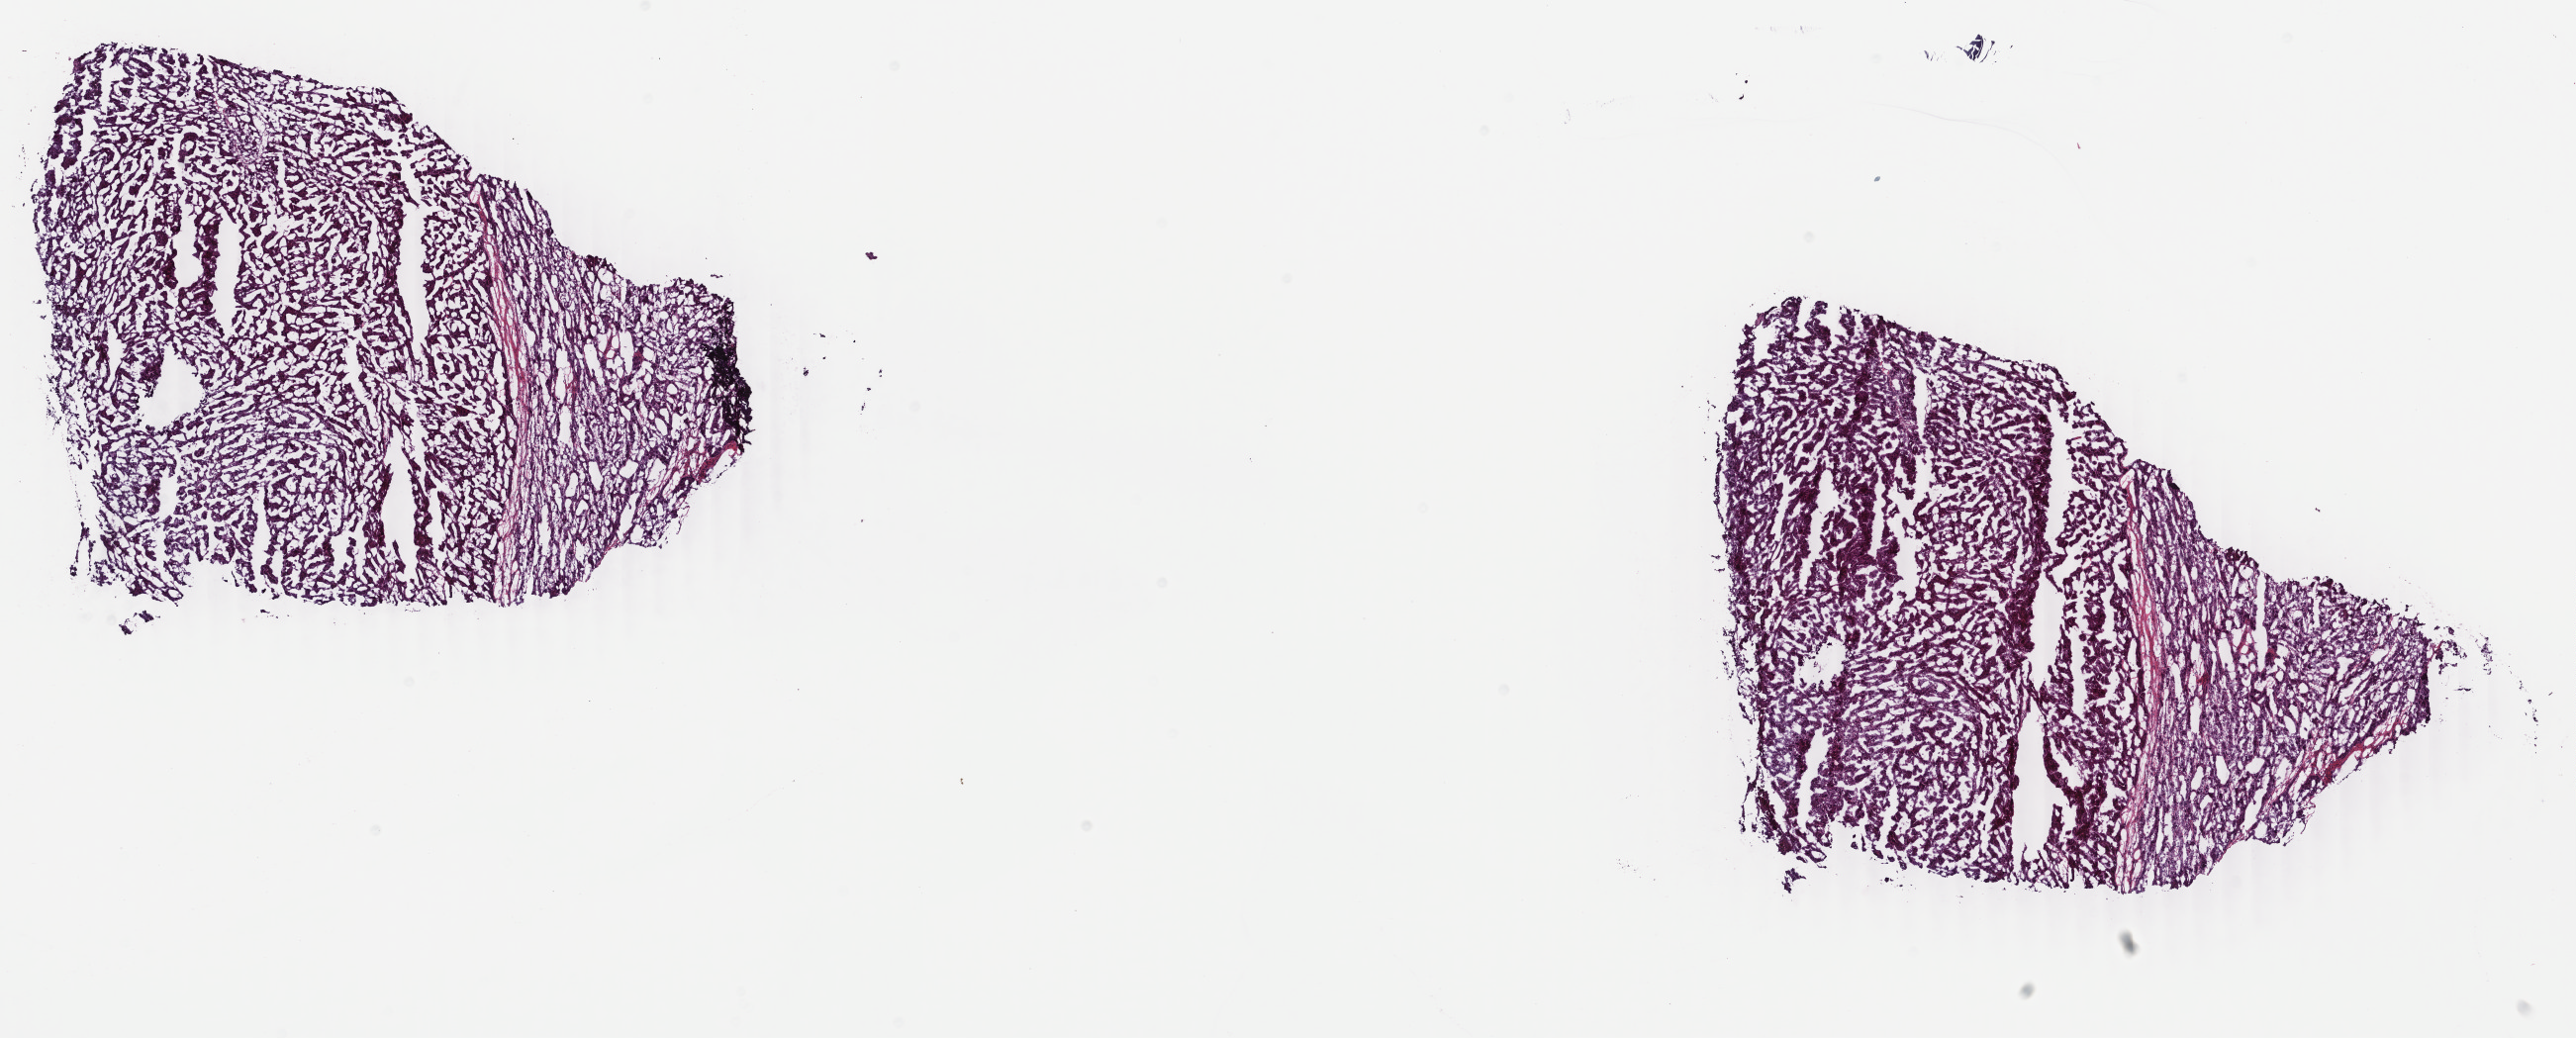
Hematoxylin and eosin (H&E) stained whole-slide image — whole scanned area (about 20.7 x 8.3 mm) shown as a low-resolution overview, frozen section, primary tumour sample from the liver. Male patient; age at initial diagnosis 68 years. Histologic grade: G3 (poorly differentiated). Slide review estimates, as recorded: tumour cells 90%, tumour nuclei 90%, normal cells 0%, stromal cells 10%, necrosis 0%. Infiltration values recorded for this section: lymphocyte infiltration 1%, monocyte infiltration 1%, neutrophil infiltration 0%.
Diagnosis: Hepatocellular carcinoma, NOS. AJCC pathologic stage: IIIA (5th edition).